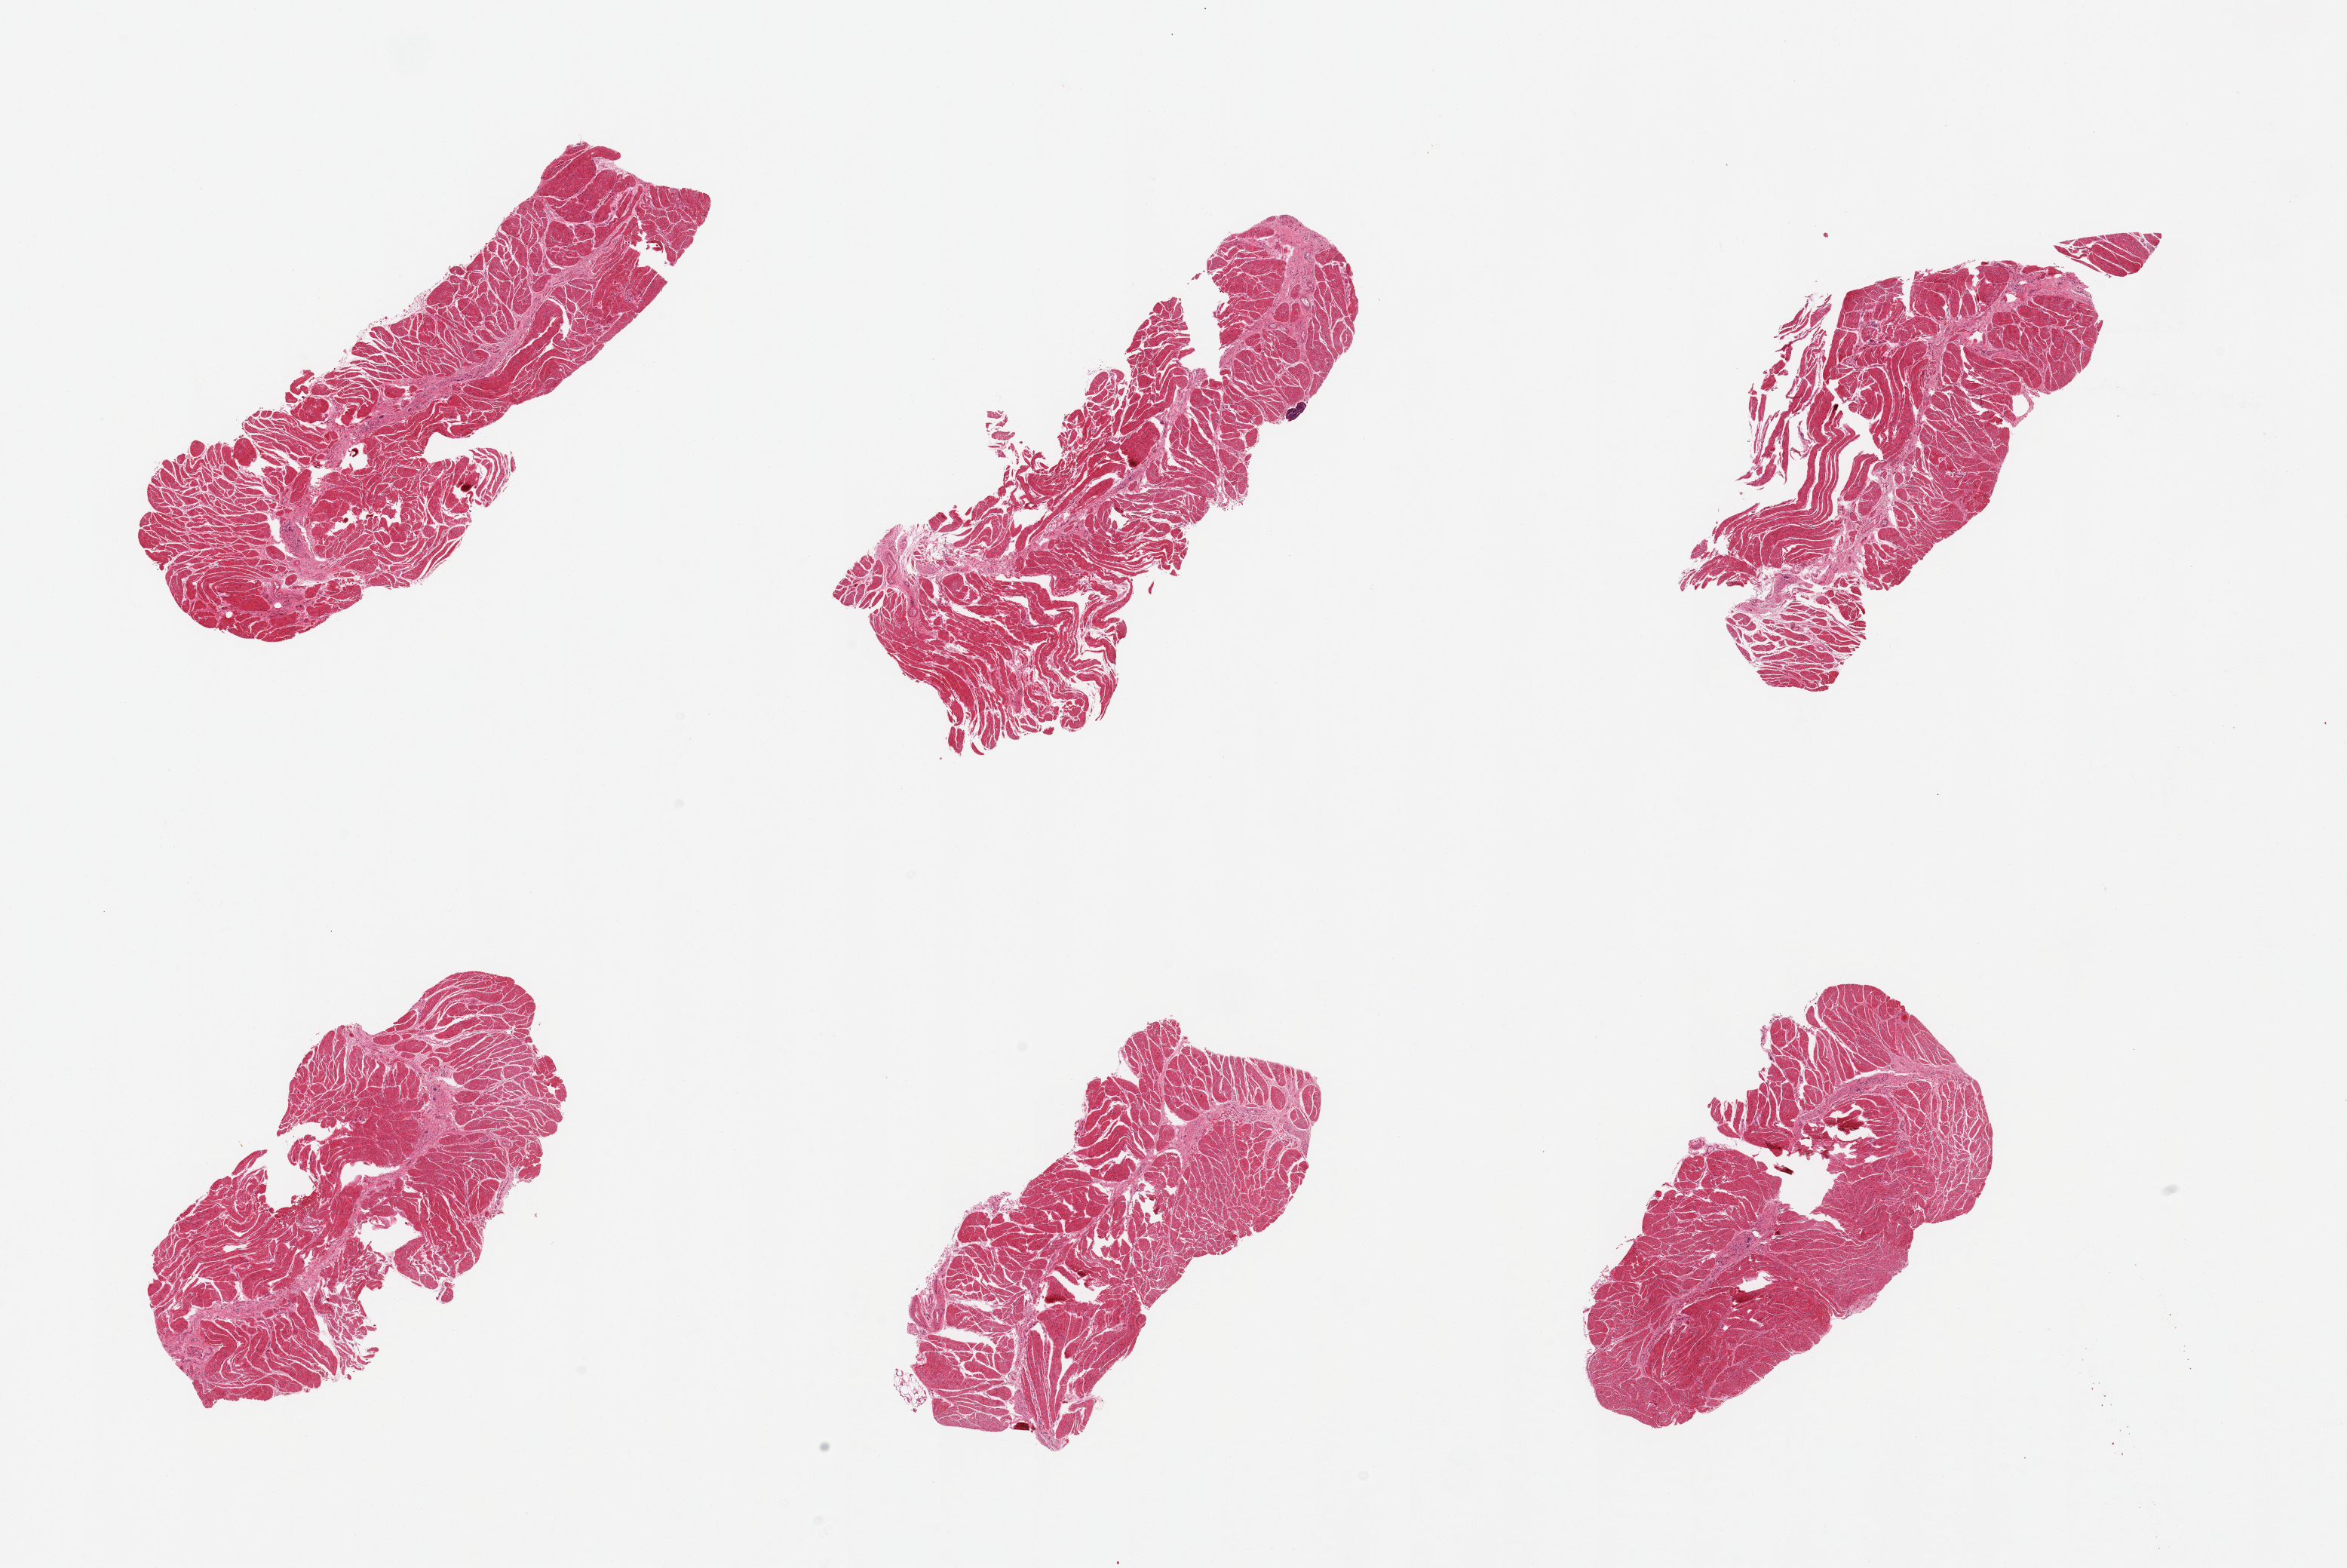
Whole-slide image, haematoxylin and eosin stain — low-resolution overview of the scanned area, about 24.6 x 16.4 mm (from a 20x scan); PAXgene-fixed paraffin-embedded (PFPE) section; section of gastroesophageal junction (target tissue); donor tissue sample.
* review note (as recorded): 6 pieces, confirmed target muscularis